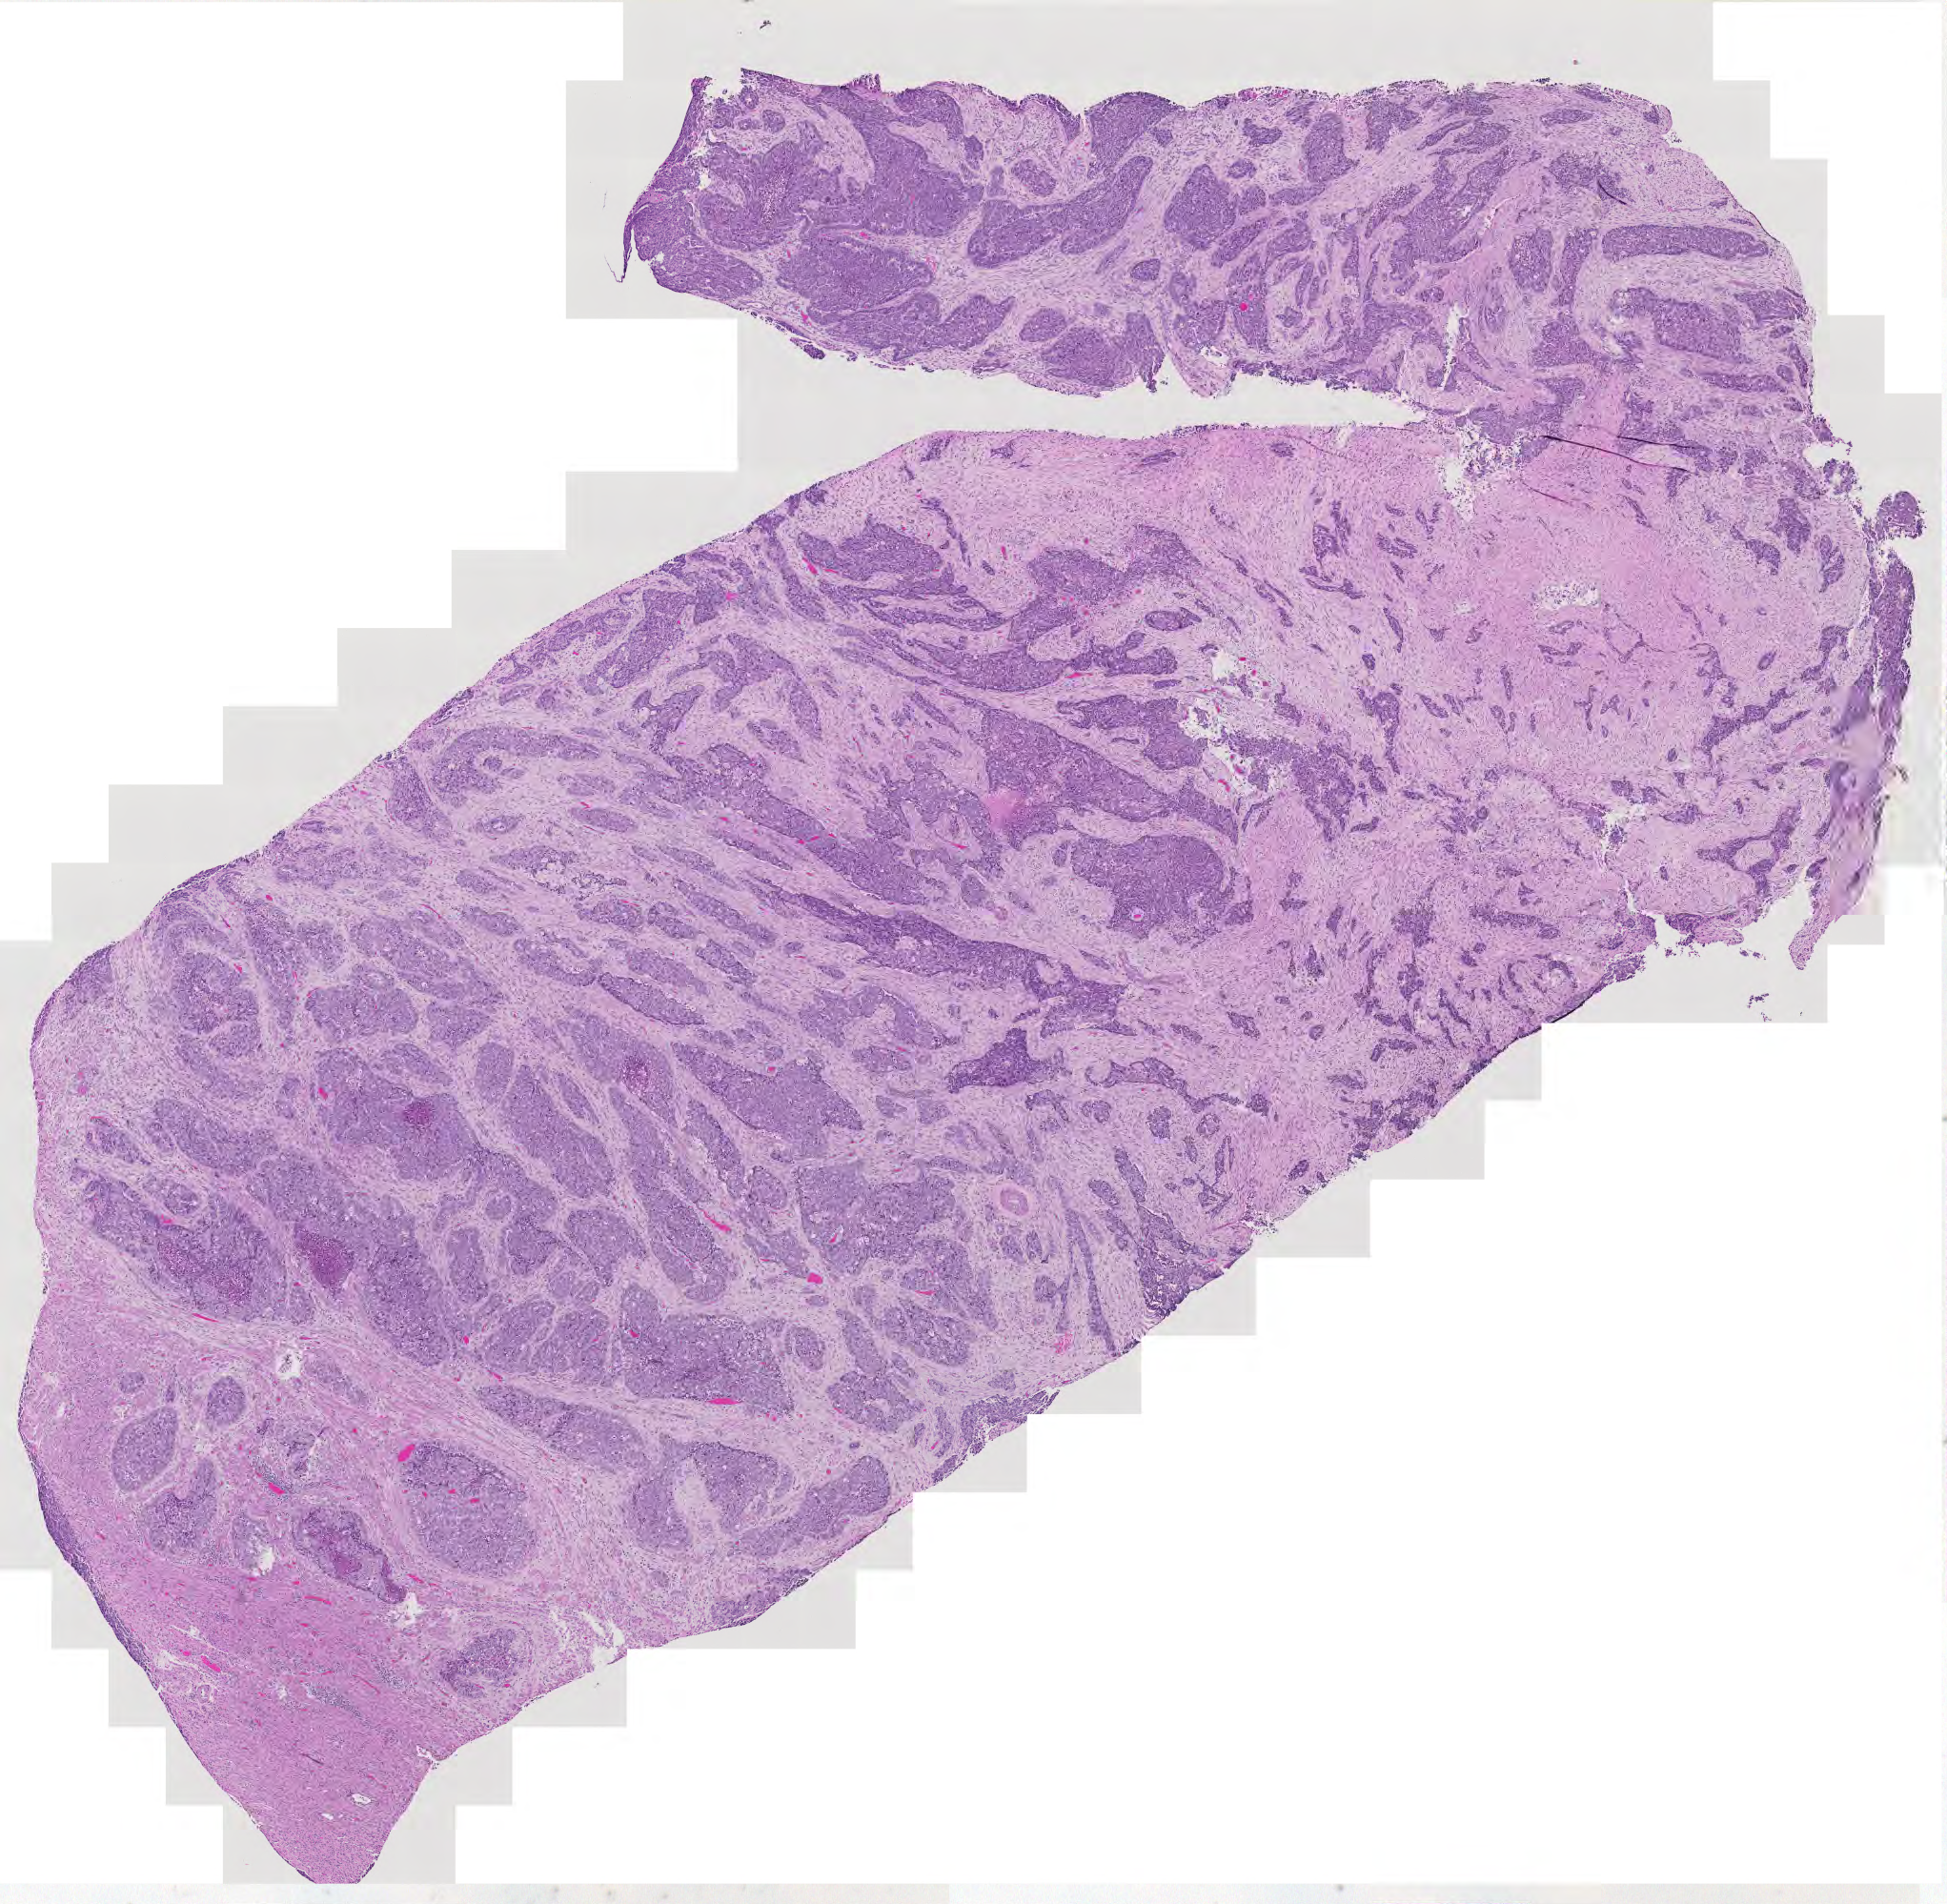
Whole-slide histology image, Hematoxylin and eosin (H&E) stained — a low-resolution overview of the entire scanned area, about 10.5 x 10.3 mm, tumour tissue sample, sampled site: uterus. Female, 65 y/o. Histologic grade: G3 (poorly differentiated). Pathologist review of this section (percent, as recorded): tumour nuclei 80%, necrosis 10%.
• diagnosis: Endometrioid adenocarcinoma, NOS
• AJCC pathologic stage: IV